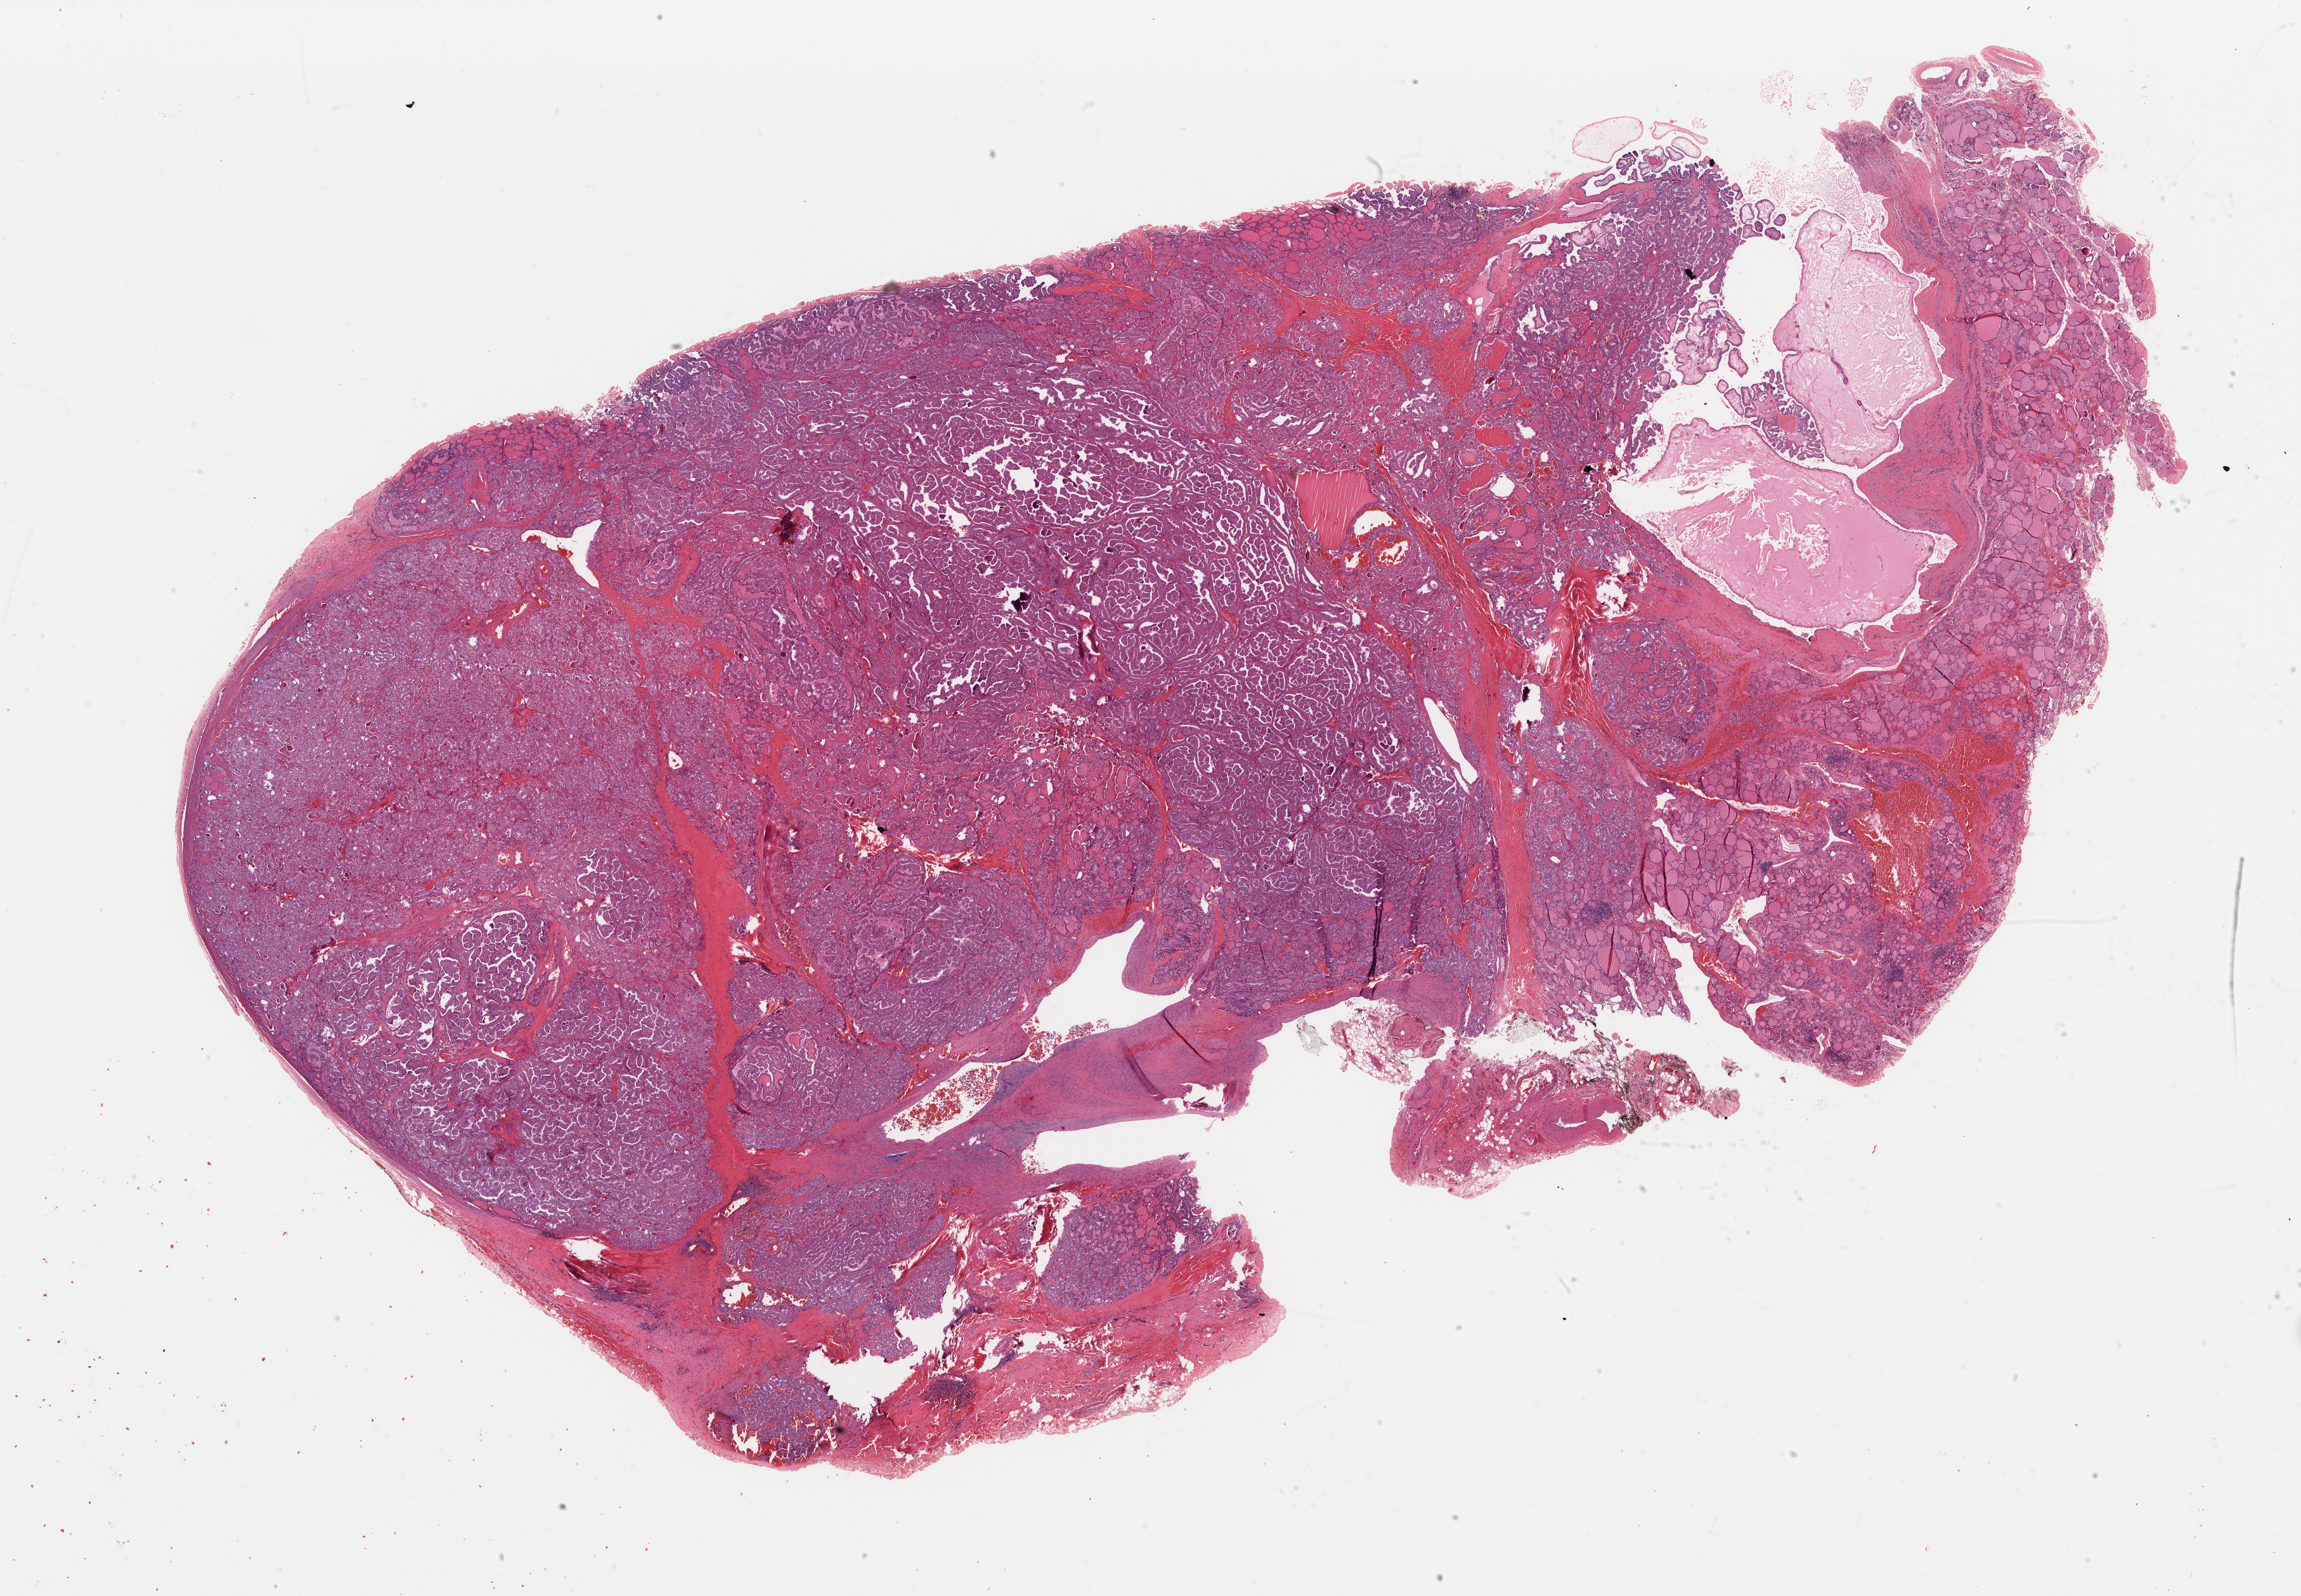
H&E whole-slide image — shown as a low-resolution overview of the whole scanned area (about 28.7 x 19.9 mm, acquisition: 40x scan). FFPE section. Primary tumour sample from the thyroid. Female, age 45 years at initial diagnosis.
Pathologic diagnosis: Papillary adenocarcinoma, NOS. AJCC pathologic stage: III (5th edition). TNM: T3 N1 M0.